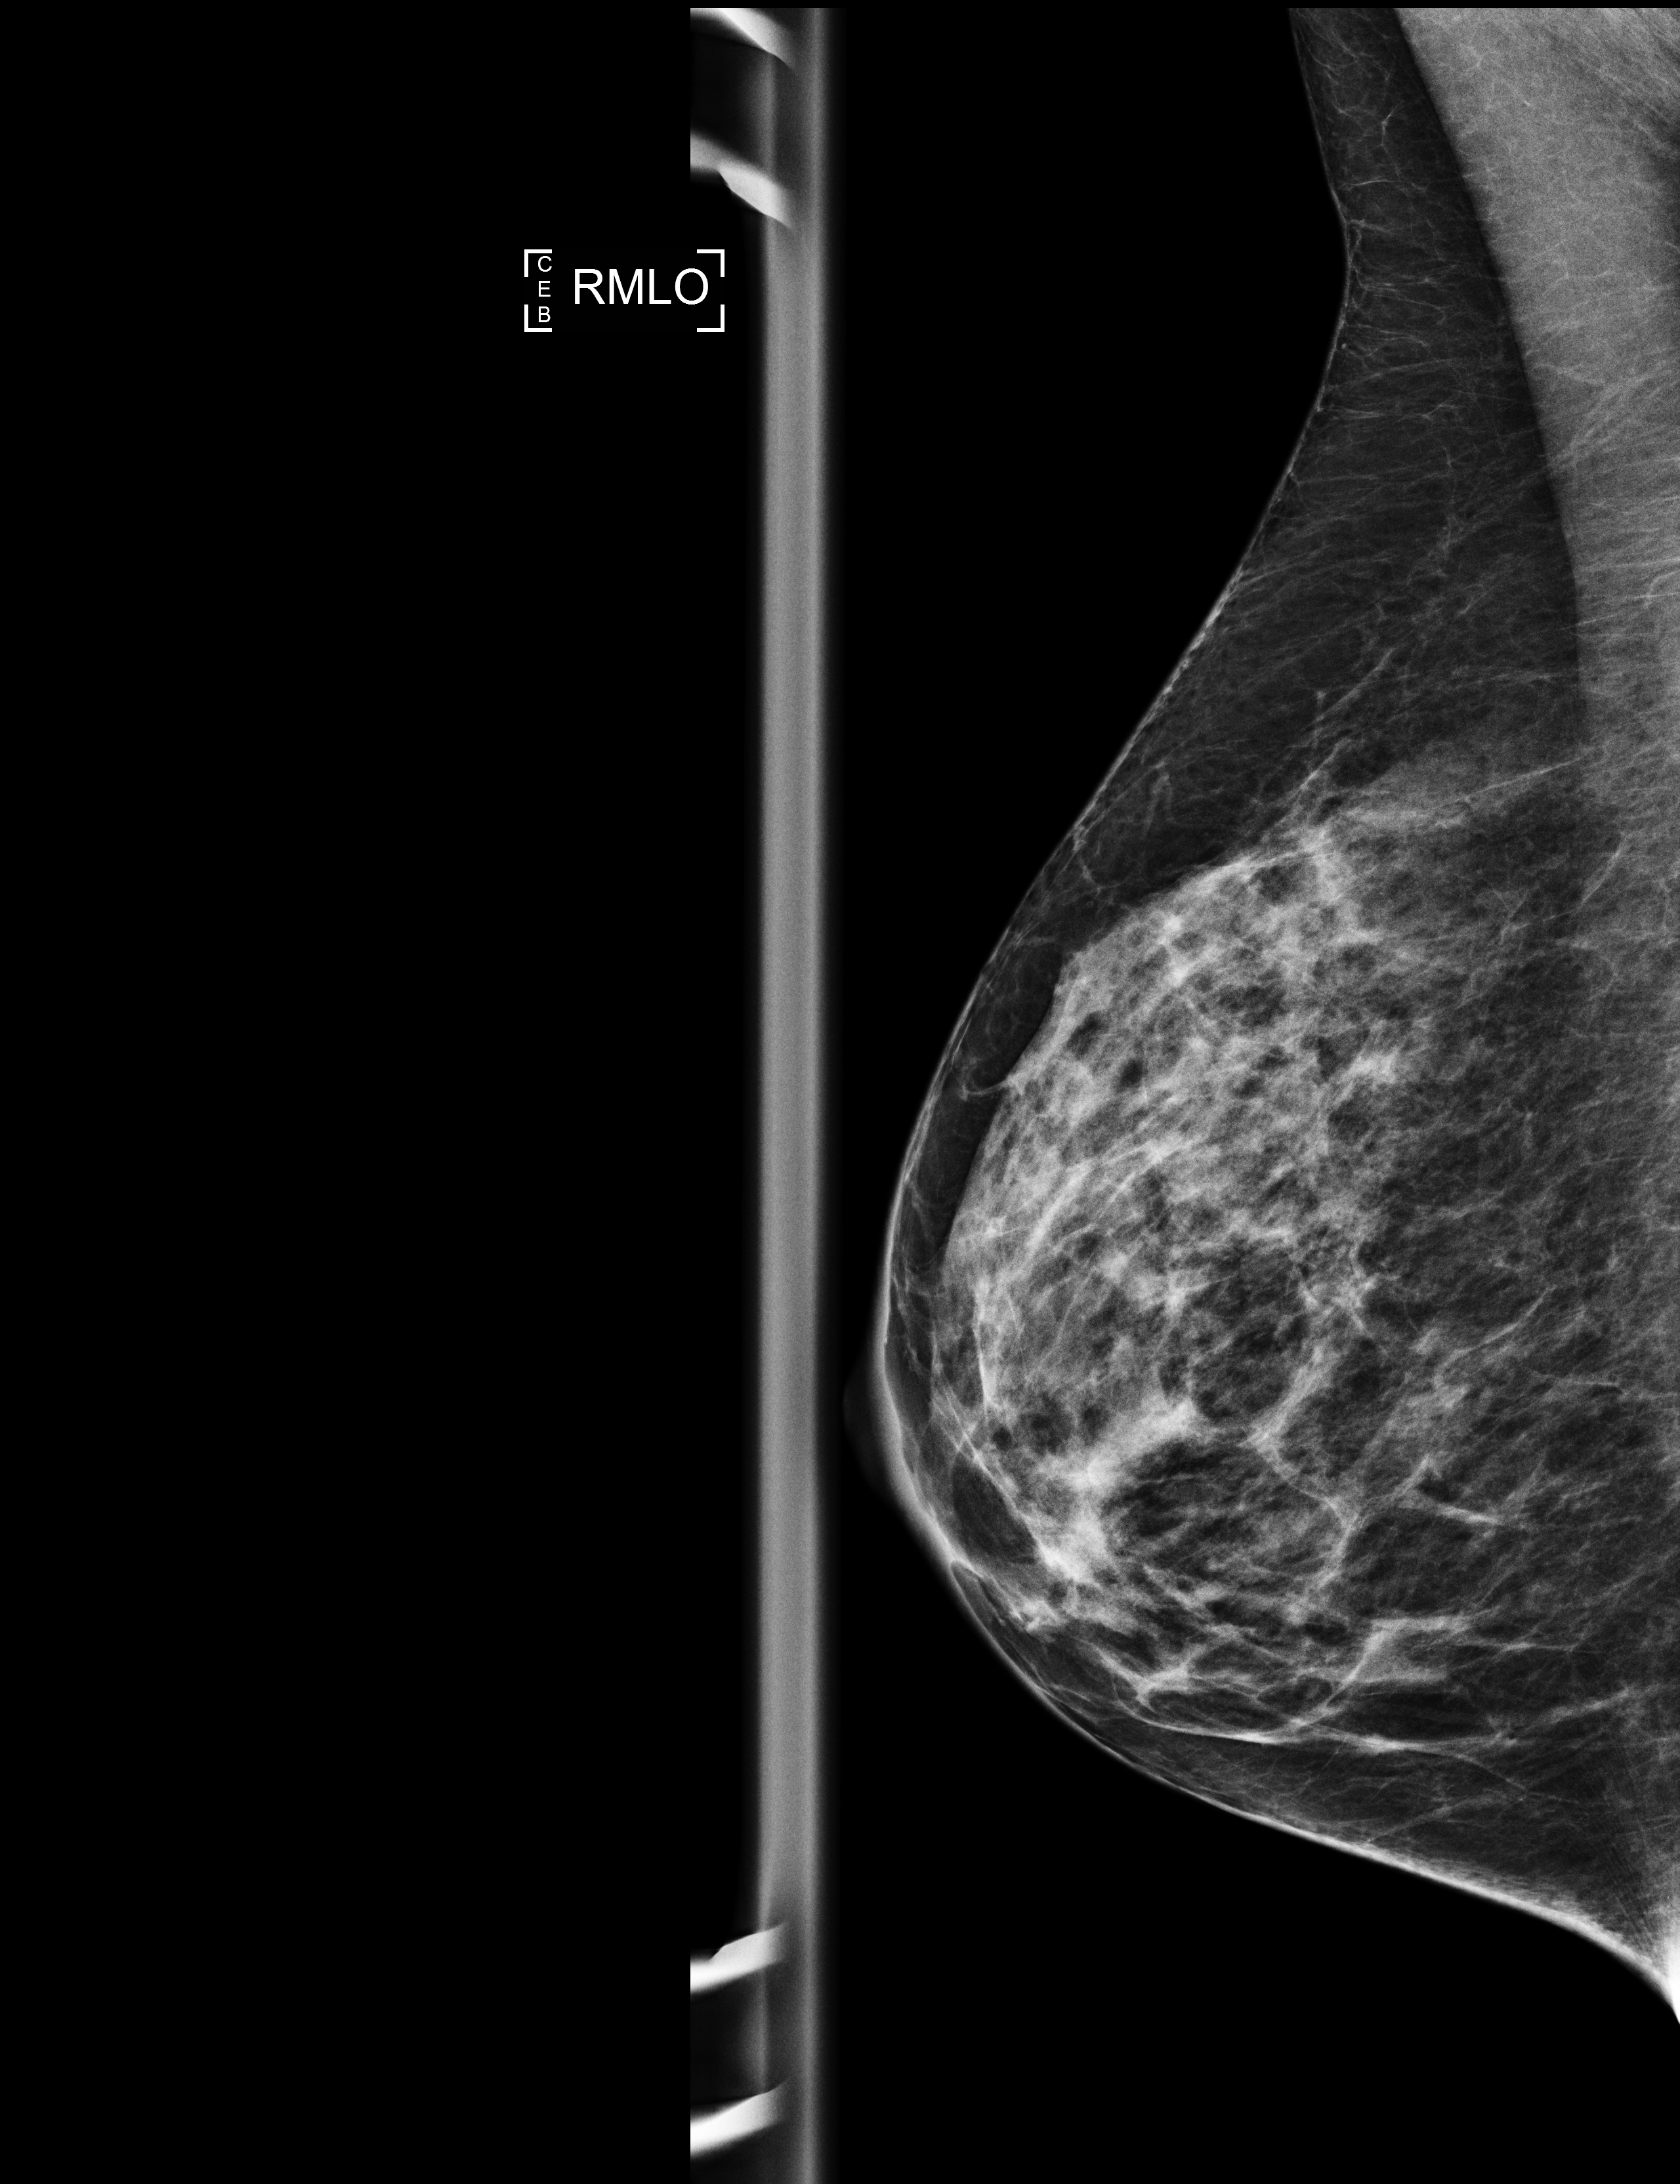
Full-field digital mammogram (FFDM); right breast; MLO view; annual screening mammography examination; compressed breast thickness 38 mm. Female patient, age 68 years.
Breast density at the screening exam (both breasts): heterogeneously dense (BI-RADS density category c). Final BI-RADS assessment for this screening round (tomosynthesis exam, both breasts): category 2. Recall: no recall after this screen.